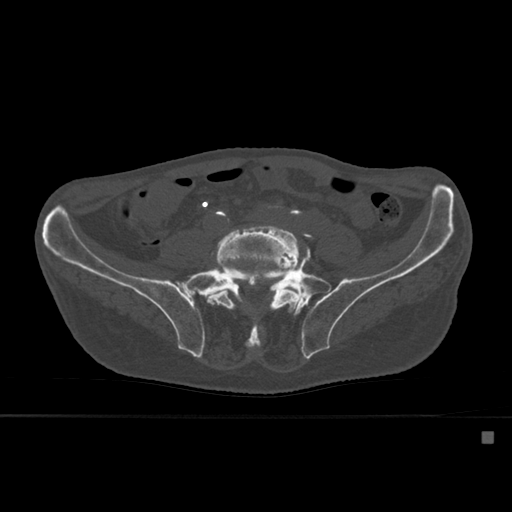
CT including the spine, one axial slice; position 169 of 527 along the scan axis; bone window (W 1800 / L 400 HU); 1.5 mm slice thickness; 512 × 512 image matrix, field of view 373 × 373 mm. Male patient, age 78 years. From the clinical record (not read from this slice): primary cancer: prostate.
Annotated regions visible in this slice (semi-automatic segmentation, software-assisted and operator-edited):
- L5 vertebra: bounding box [x1, y1, x2, y2] px = [206, 227, 303, 349]